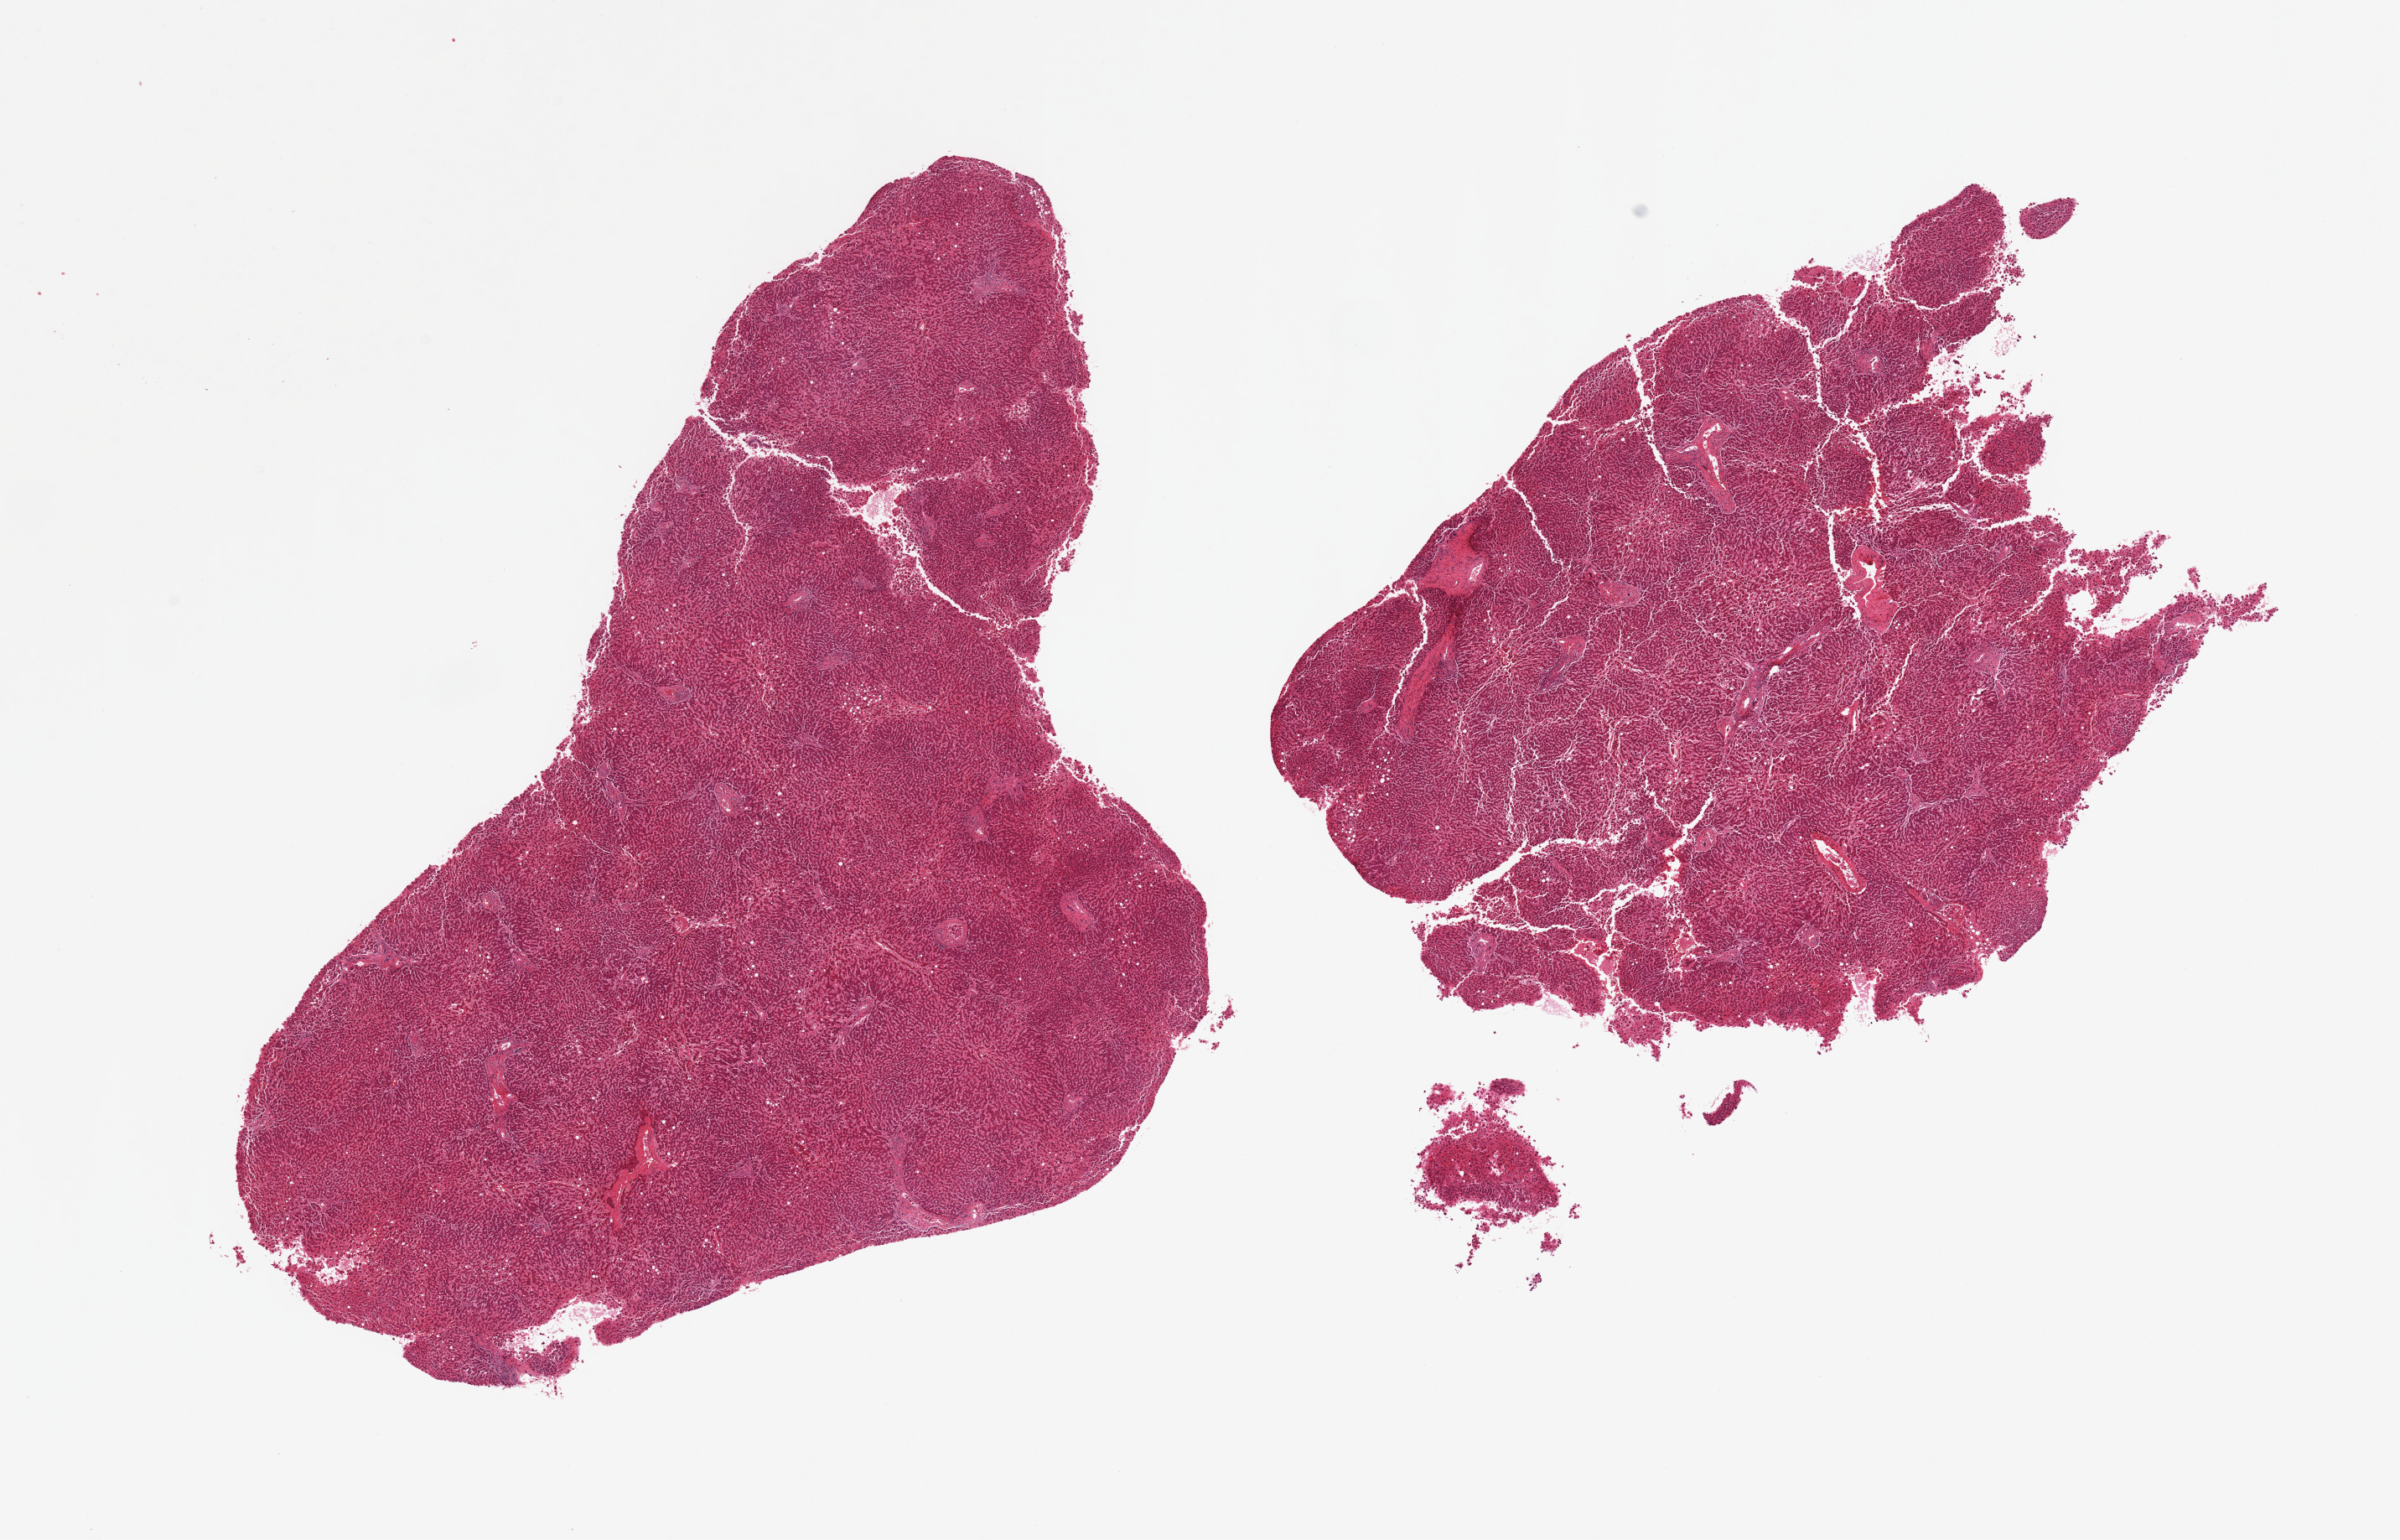
Whole-slide image, H&E stain, shown as a low-resolution overview of the whole scanned area (about 22.6 x 14.5 mm). PAXgene-fixed paraffin-embedded (PFPE) section. Target tissue: liver. Donor tissue sample. Donor: male.
* pathologist's review note for this sample: 2 pieces, moderately advanced passive congestion